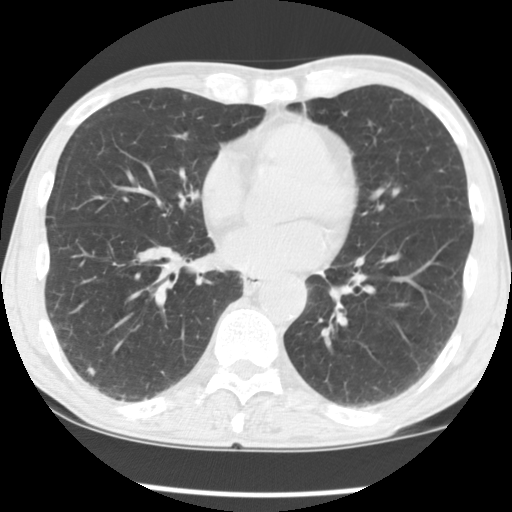
Low-dose screening chest CT, one axial slice; slice 57 of 135 in the series (ordered by position); reconstruction kernel STANDARD; lung window (W 1500 / L -600 HU); 2.5 mm slice thickness; 512 × 512 image matrix, field of view 310 × 310 mm.
Structures marked on this image (manually delineated by an expert):
- lesion 1 (tumor, lower lobe of right lung): bounding box <87,367,96,376> (left, top, right, bottom; pixels)